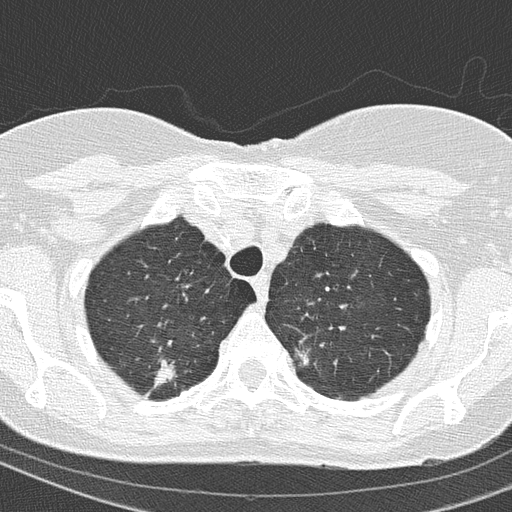
Chest CT (low-dose screening protocol), one axial image, baseline annual screen, lung window (W 1500 / L -600 HU), lung (sharp) reconstruction kernel (B50f), 512 × 512 image matrix. Female, age 67 years at enrolment. Current smoker at enrolment.
• Lesion marked by an expert reader, bounding box [x1, y1, x2, y2] px = [135, 348, 195, 399].
• The exam's reader record, not a measurement of the box and not confirmed to be the same lesion: non-calcified nodule or mass ≥4 mm, right upper lobe, 15 × 14 mm, spiculated (stellate) margins, soft tissue attenuation.
• Participant outcome: lung cancer diagnosed 63 days after this screen — adenocarcinoma, NOS, right upper lobe, moderately differentiated (G2), stage IA (AJCC 6th edition), 14 mm at pathology.